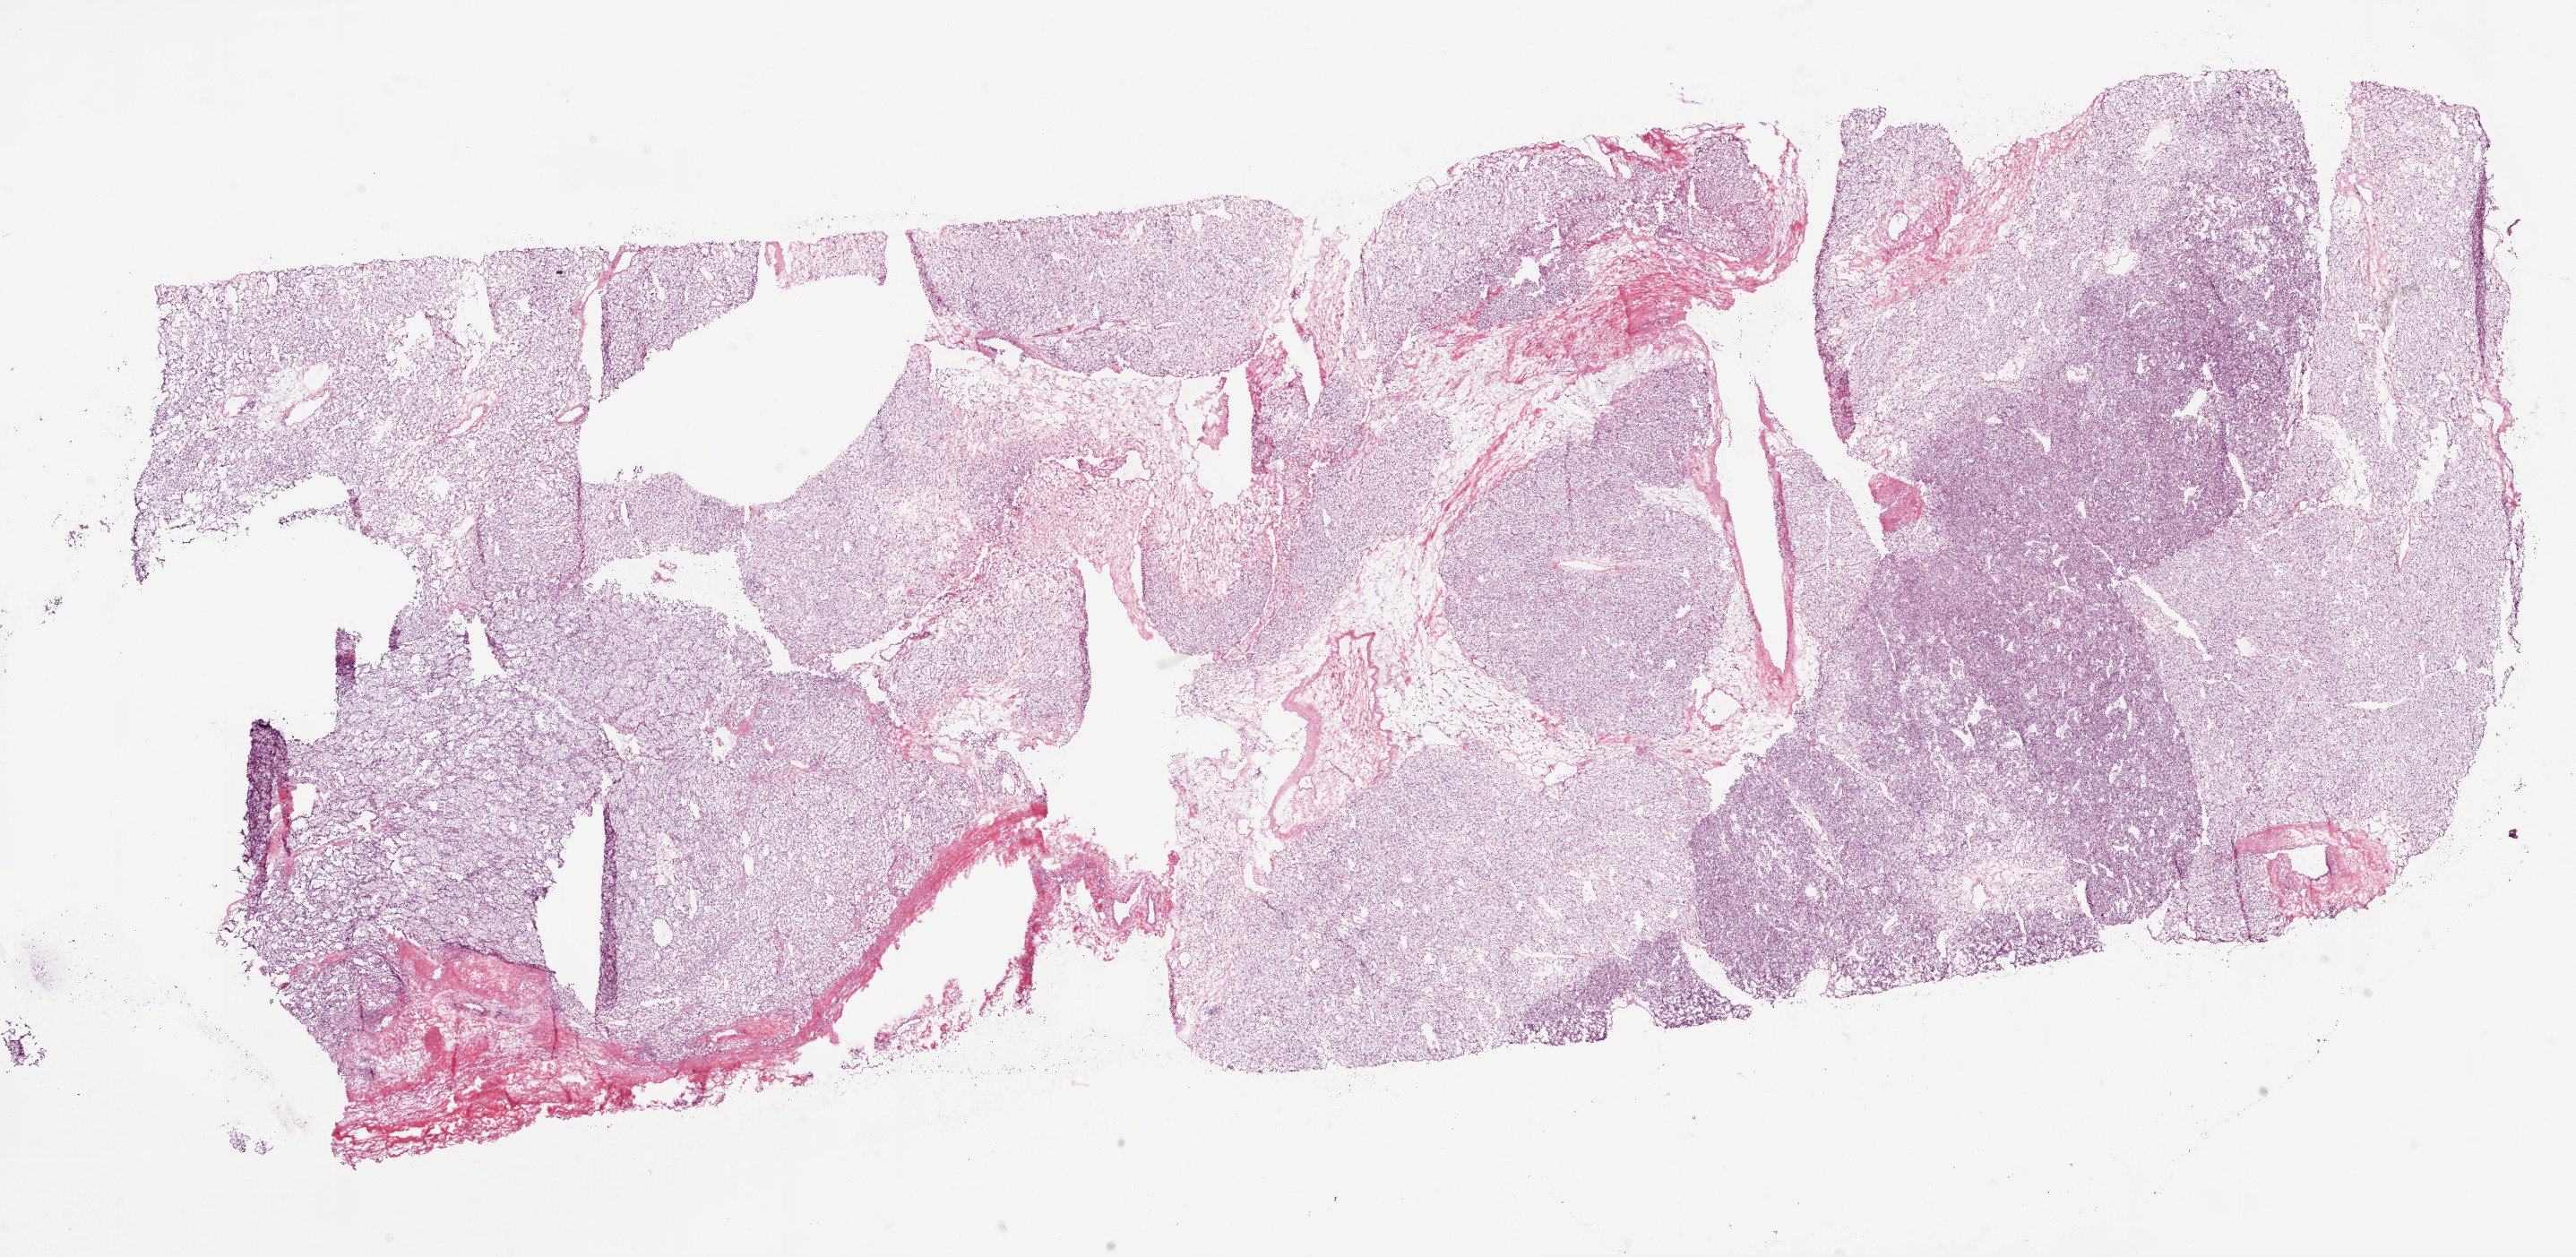
Whole-slide histology image, H&E-stained — a low-resolution overview of the entire scanned area, about 23.1 x 11.3 mm (slide scanned at 20x), frozen section, kidney, primary tumour sample. Female, age 60 years at initial diagnosis. Histologic grade: G3 (poorly differentiated). Composition of this section per pathologist review: tumour cells 90%, tumour nuclei 85%, normal cells 0%, stromal cells 10%, necrosis 0%.
AJCC pathologic stage: IV (7th edition). Lymph nodes positive (case pathology): 0 of 13 examined. Laterality: left. Diagnosis: Clear cell adenocarcinoma, NOS.